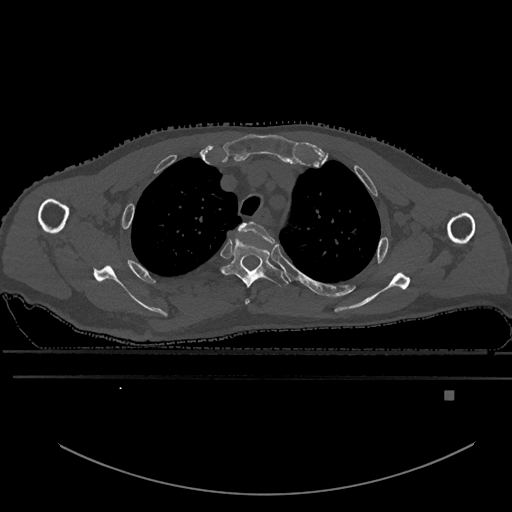
CT including the spine, one axial slice; position 460 of 969 along the scan axis; bone window (W 1800 / L 400 HU); 0.5 mm slice thickness; 512 × 512 image matrix, field of view 456 × 456 mm. Patient: male, 82 years. Case-level facts recorded for this patient, not image findings: primary cancer: prostate.
Structures marked on this image (semi-automatically segmented with operator editing):
- T2 vertebra: bounding box (x1, y1, x2, y2) in pixels: (238, 221, 276, 305)
- T3 vertebra: (222, 239, 289, 288)